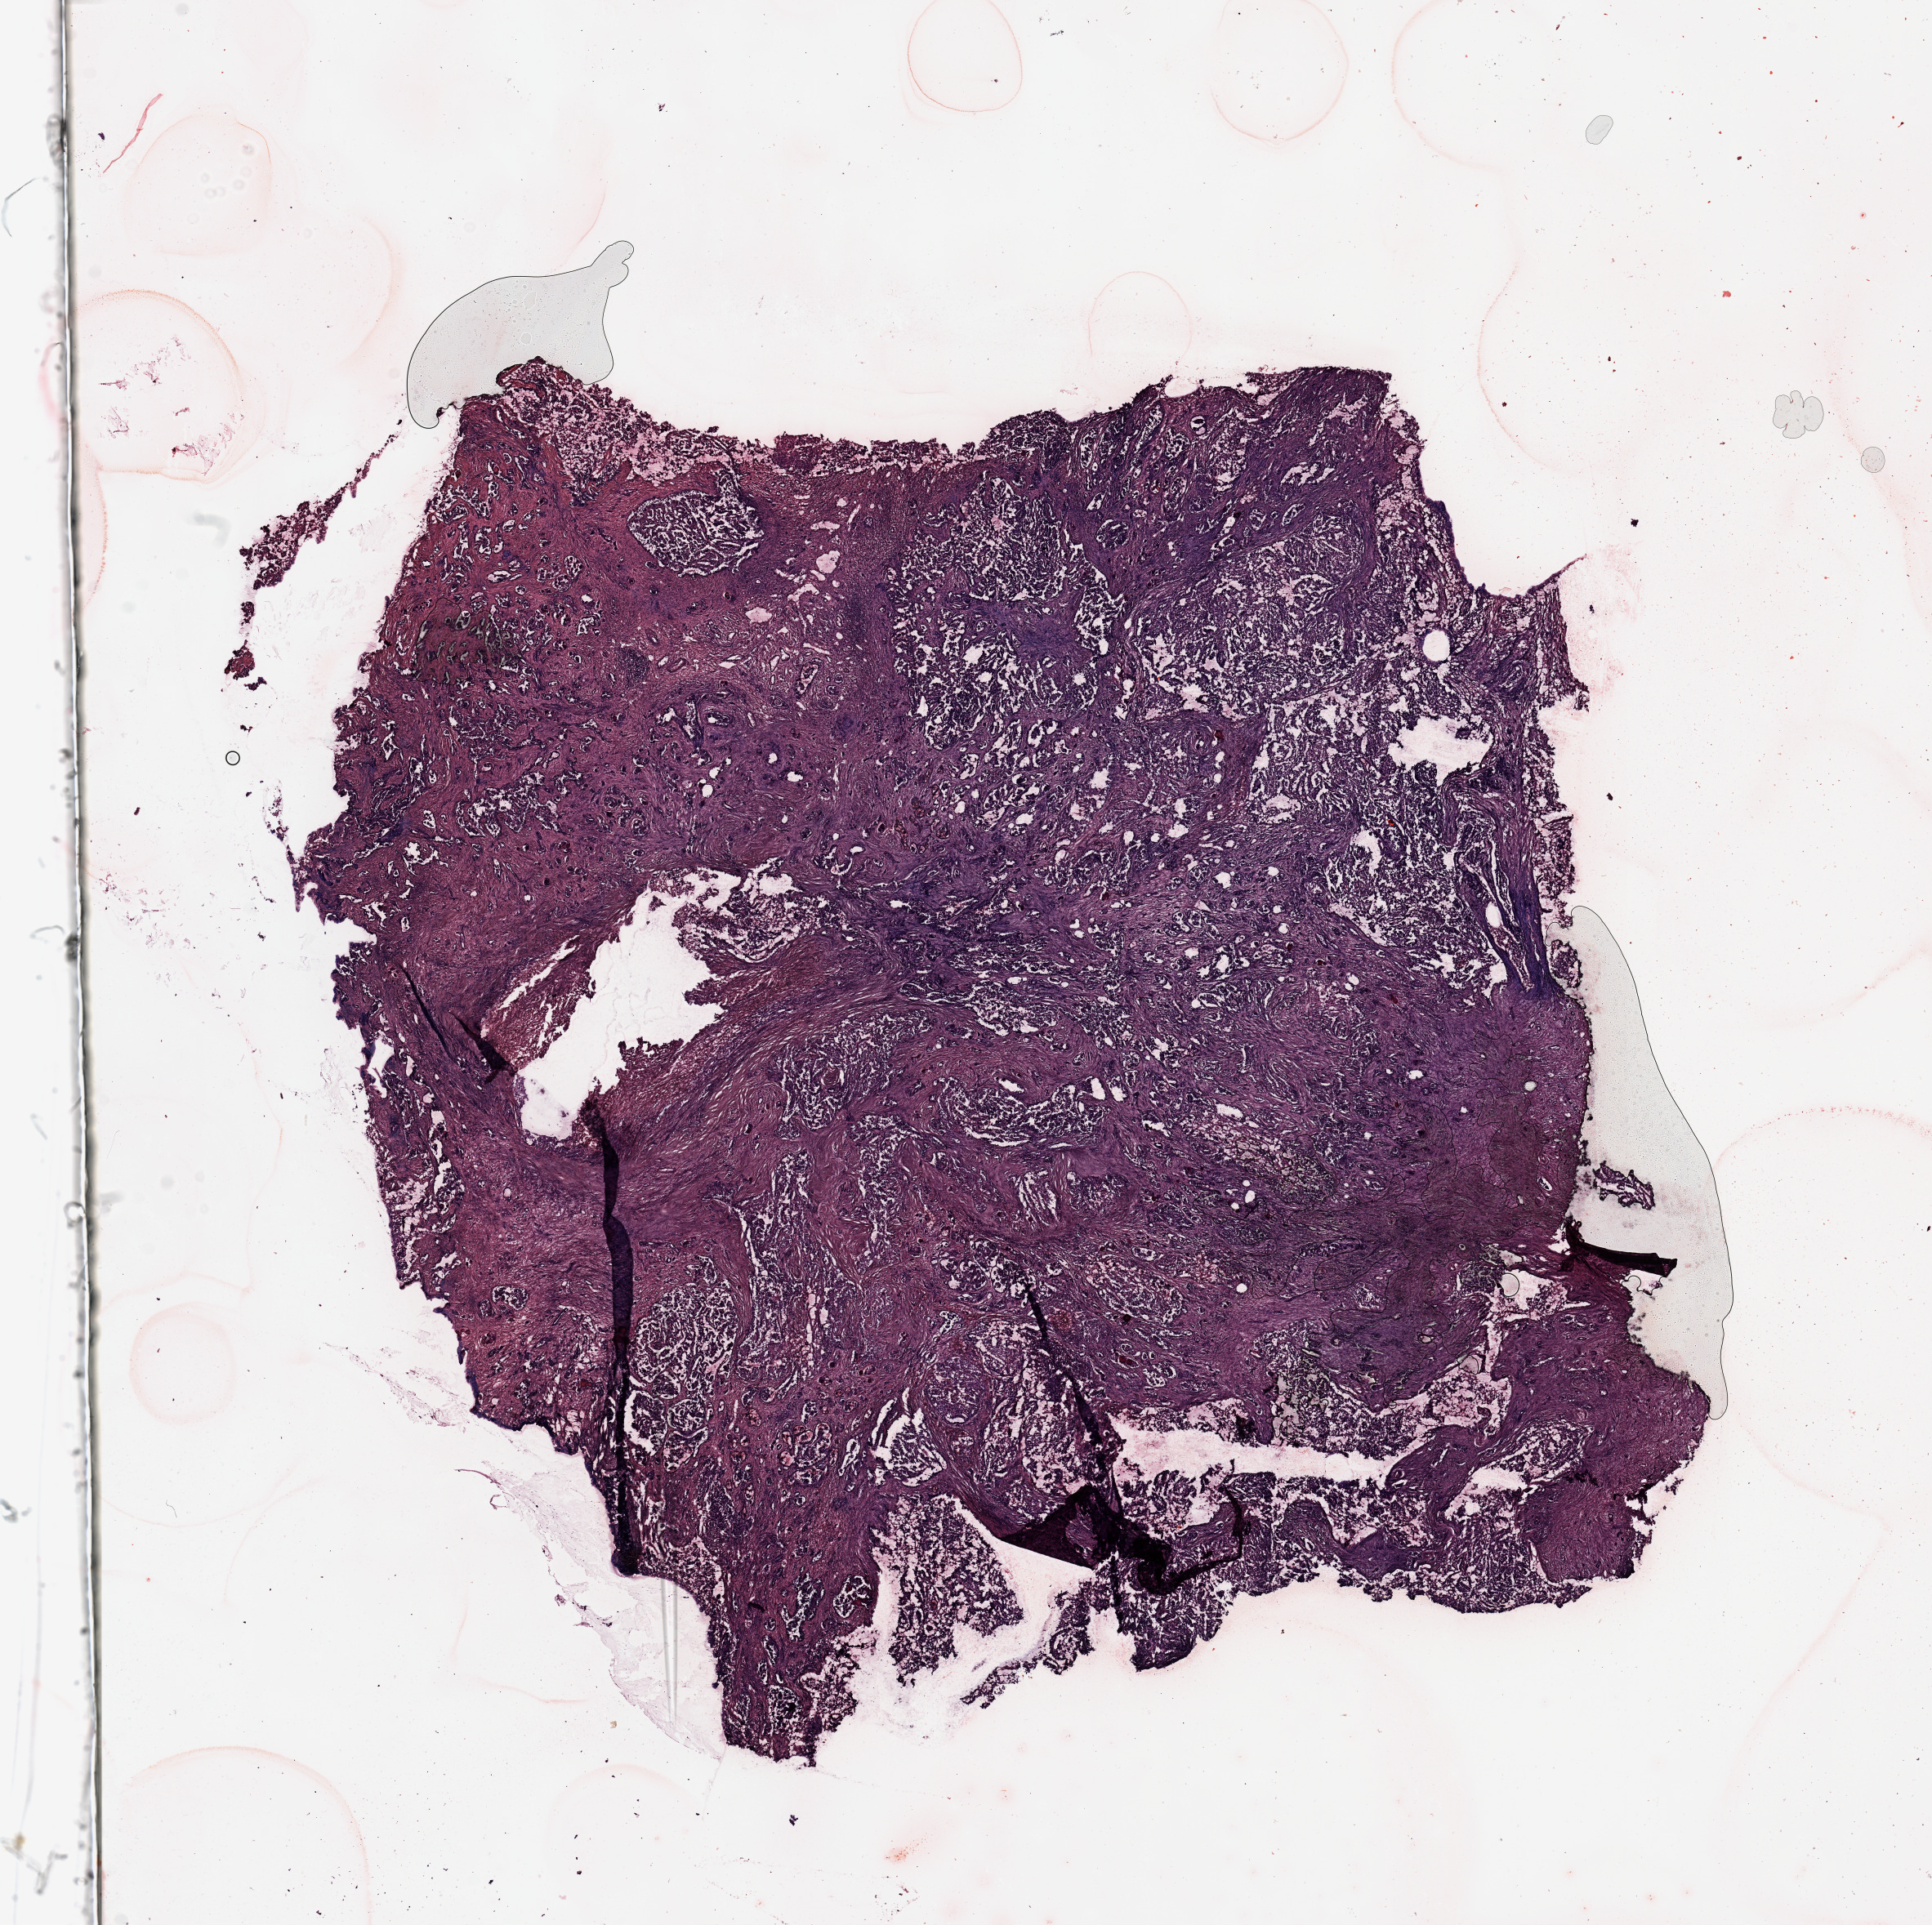
Whole-slide histology image, H&E — low-resolution overview of the scanned area, about 18.7 x 18.6 mm. Kidney, tumour tissue. Patient: male, age 72 years. Histologic grade: G3 (poorly differentiated).
- AJCC pathologic stage: III
- histologic diagnosis: Renal cell carcinoma, NOS
- primary tumour site (as recorded): upper pole